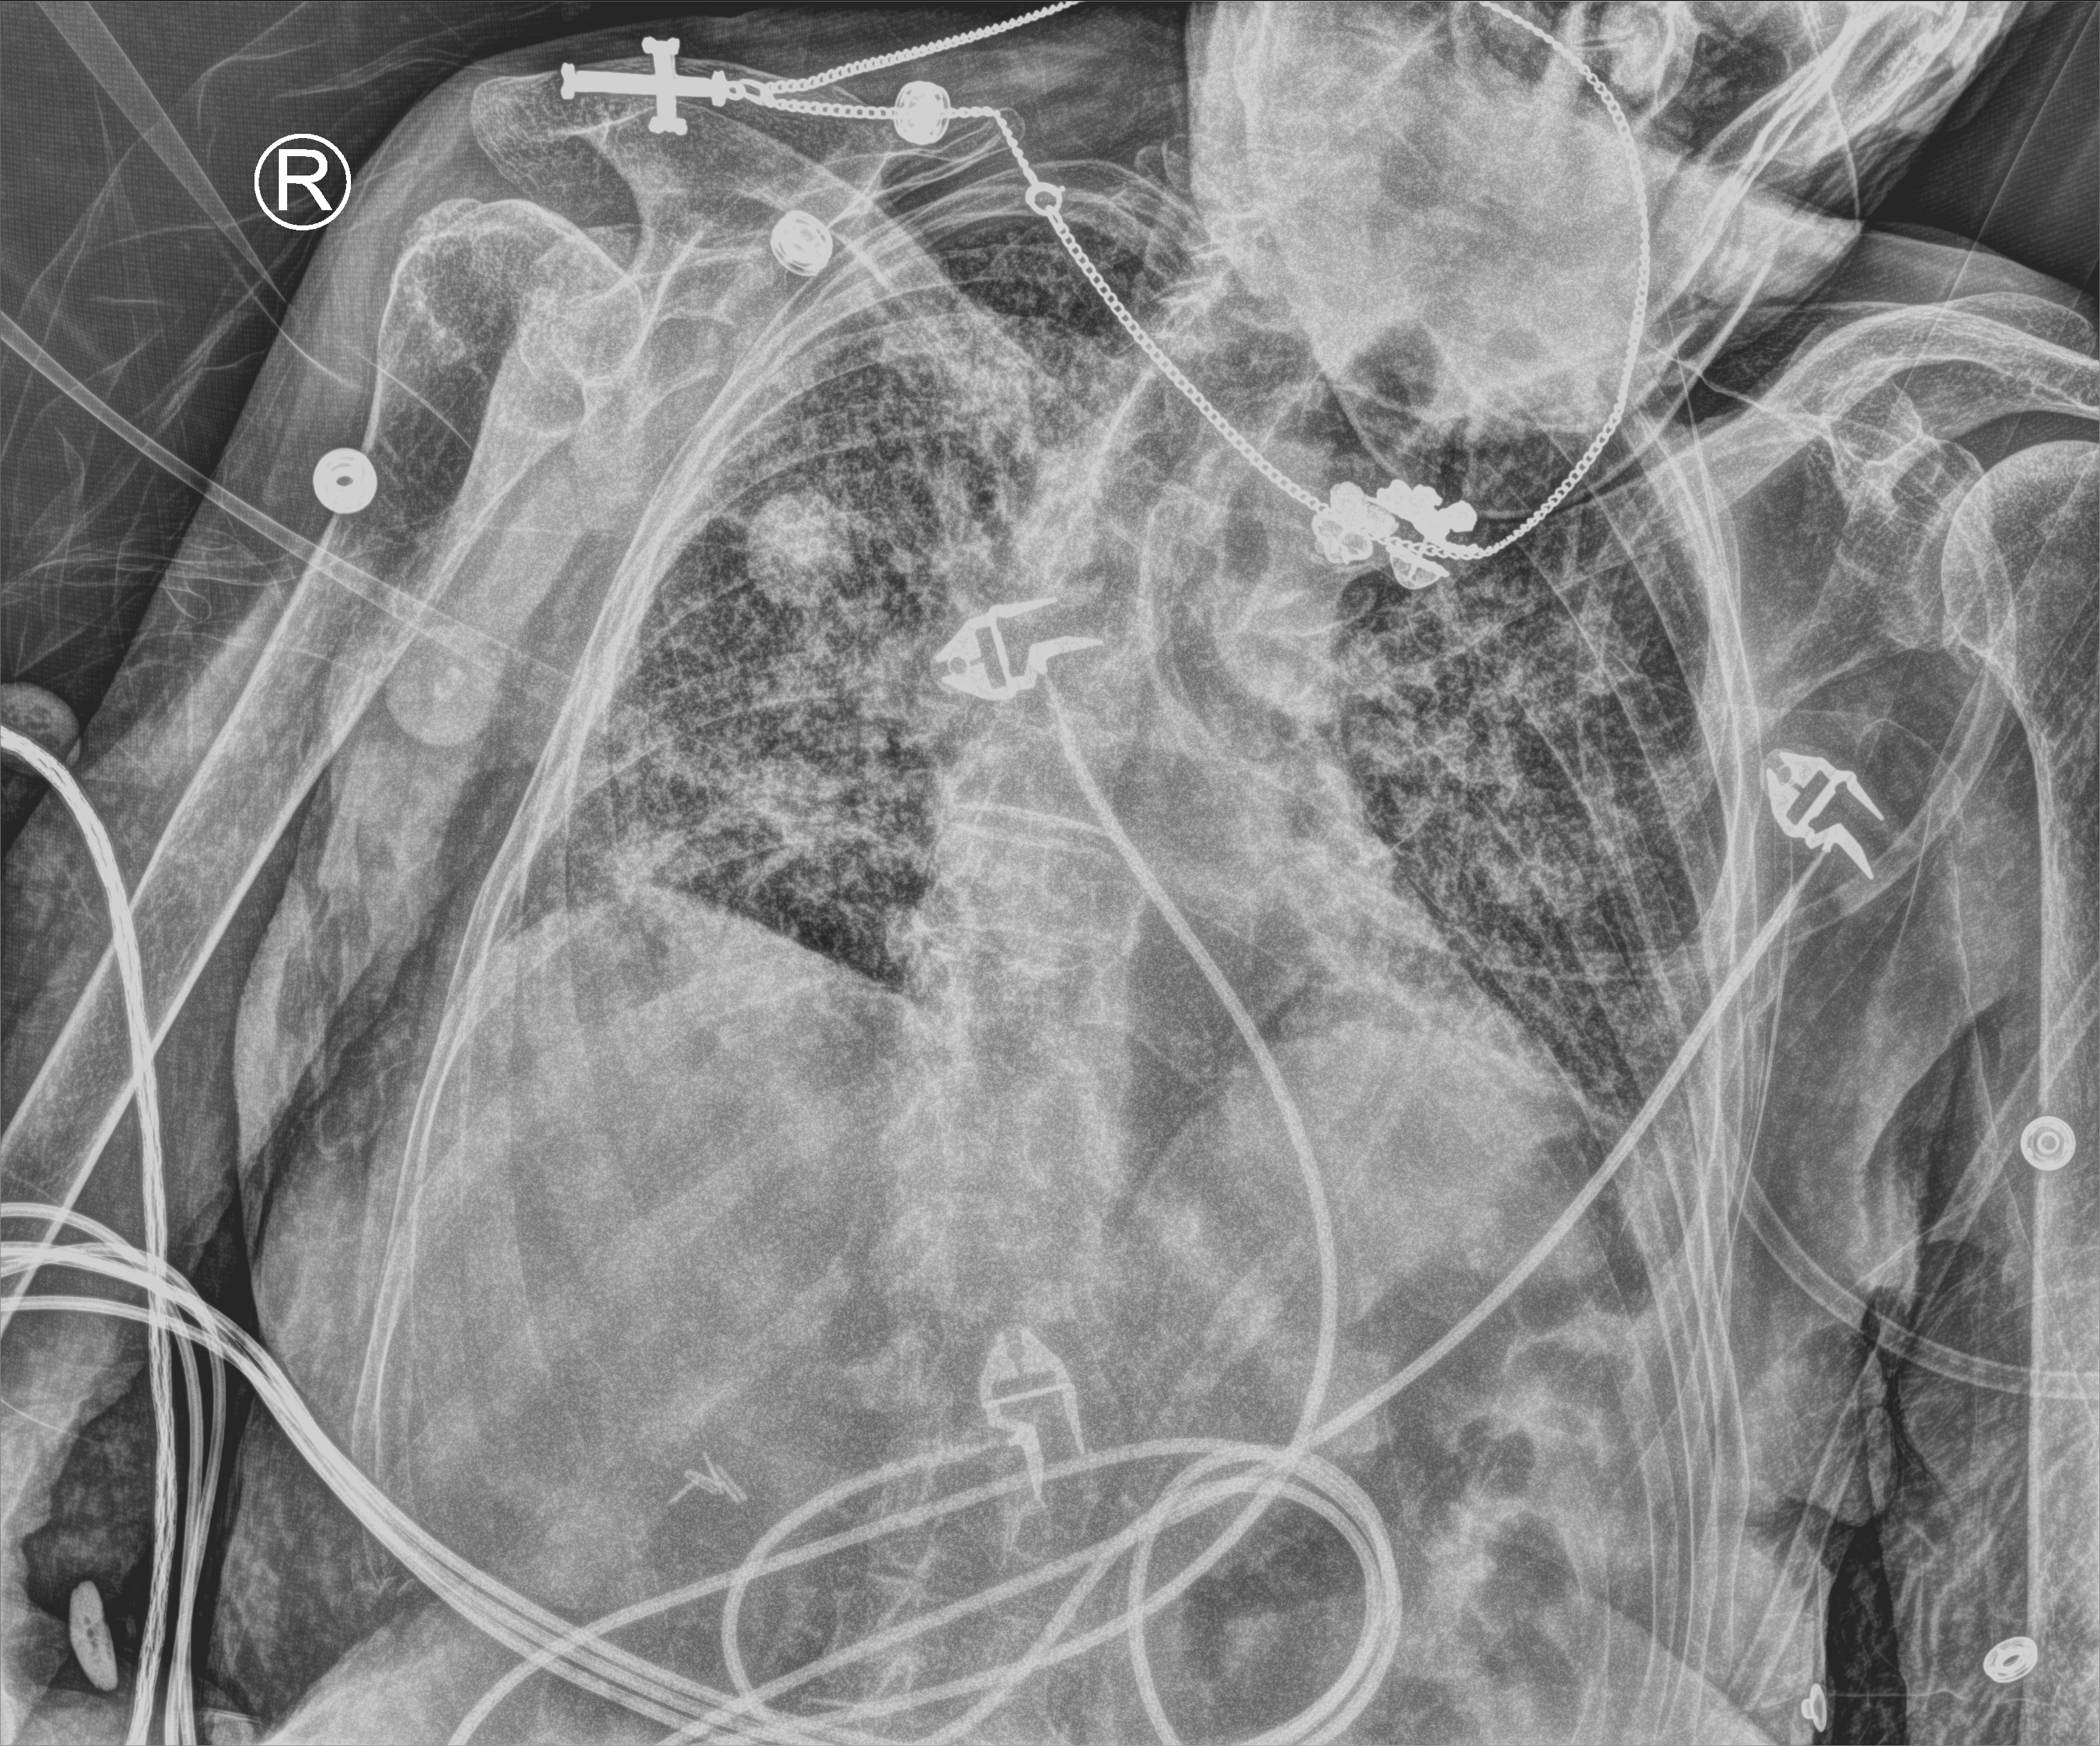
Bedside chest radiograph (computed radiography); anteroposterior (AP) projection. Patient hospitalised with COVID-19; female, aged 75–90 years.
Admission-level facts for this patient (not findings on this image; timing relative to this image not recorded):
- chronic kidney disease (admission record): no
- admitted to intensive care during this hospital stay: no